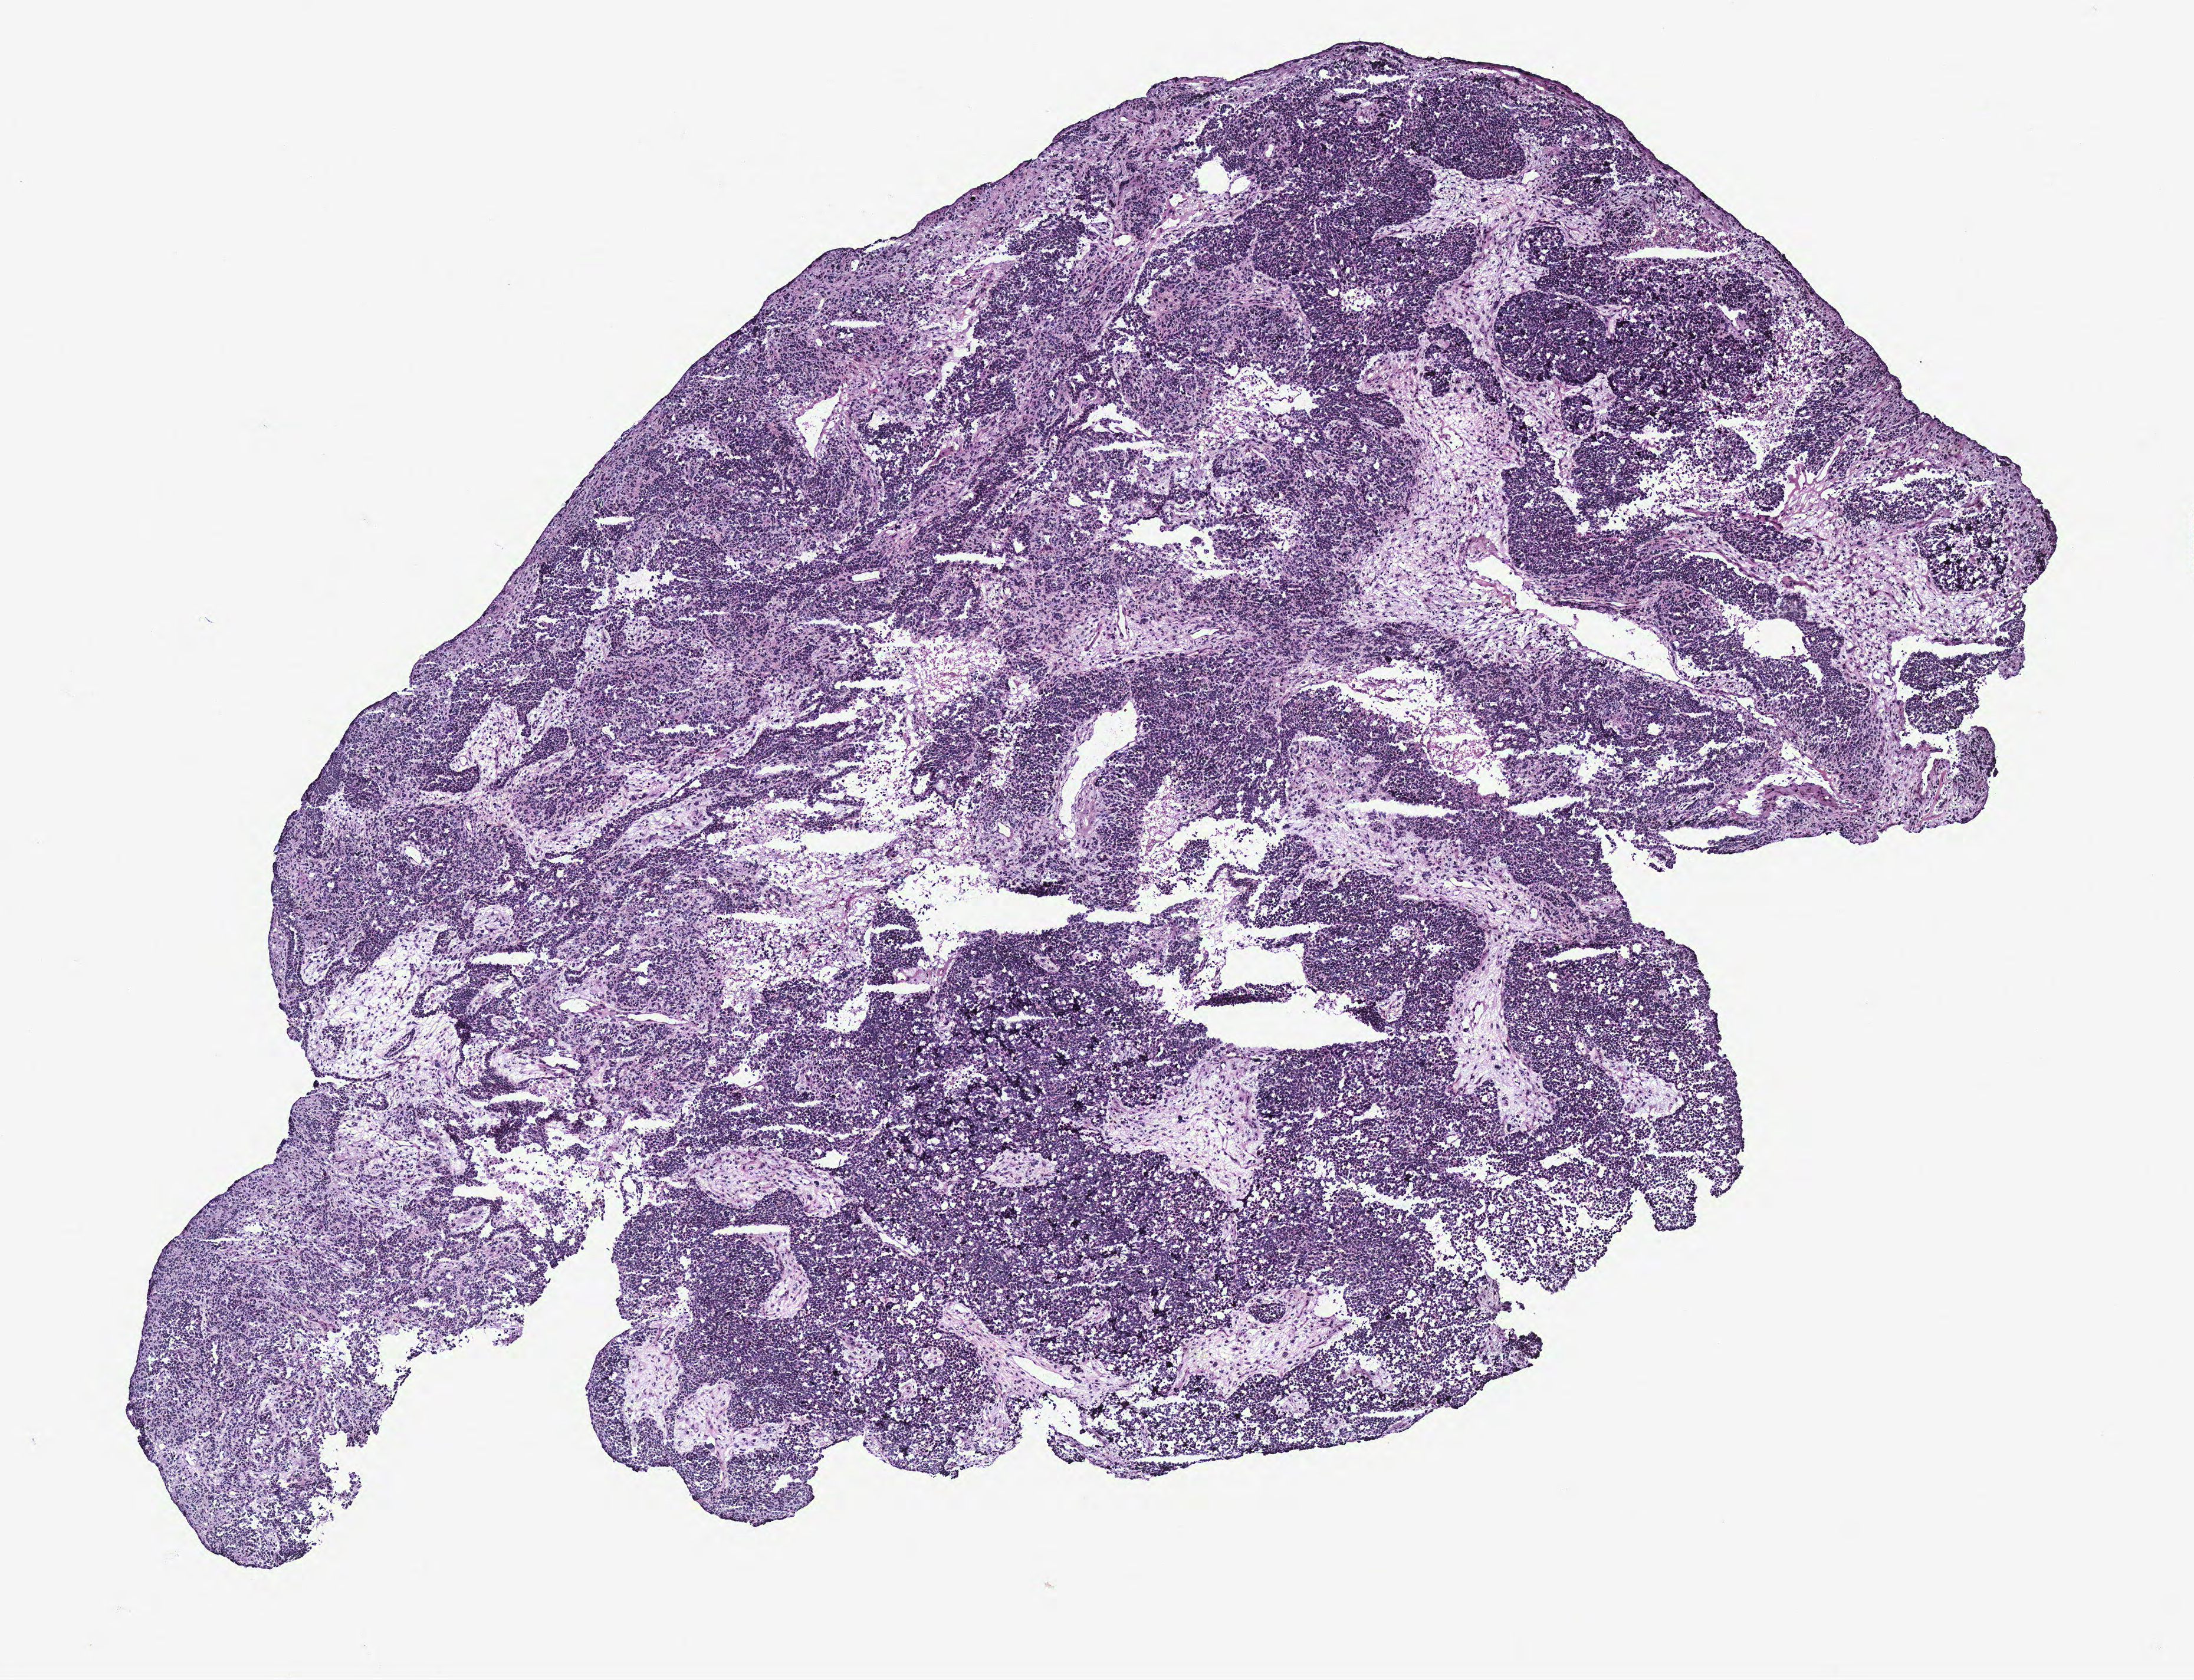
Hematoxylin and eosin (H&E) stained whole-slide image, a low-resolution overview of the entire scanned area, about 7.4 x 5.7 mm, ovary, tissue type not recorded. Patient sex: female.
• patient diagnosis: Serous adenocarcinoma, NOS